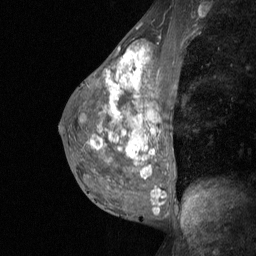
Breast MRI (dynamic contrast-enhanced), one sagittal slice. Position 35 of 64 along the scan axis. Dynamic contrast-enhanced study with each time point stored as its own series, time point 2 of 3 at this slice position (early post-contrast, ordered by acquisition time). 1.5 T. TE 4.8 ms, TR 27 ms. 2 mm slice thickness. 256 × 256 image matrix, field of view 200 × 200 mm. Female patient, age 36 years. Case-level facts recorded for this patient, not image findings: setting: breast cancer imaged before/during neoadjuvant chemotherapy; receptor status: HR-positive, HER2-negative.
Outlined on this slice (semi-automatically segmented with operator editing):
- analysis volume of interest (the breast-tissue region the enhancement analysis was run in; not a lesion): box from (x=73, y=45) to (x=187, y=210) px
- tumour enhancement mask (voxels above the 90 % enhancement threshold inside the analysis volume of interest): (x=131, y=154)–(x=146, y=169)